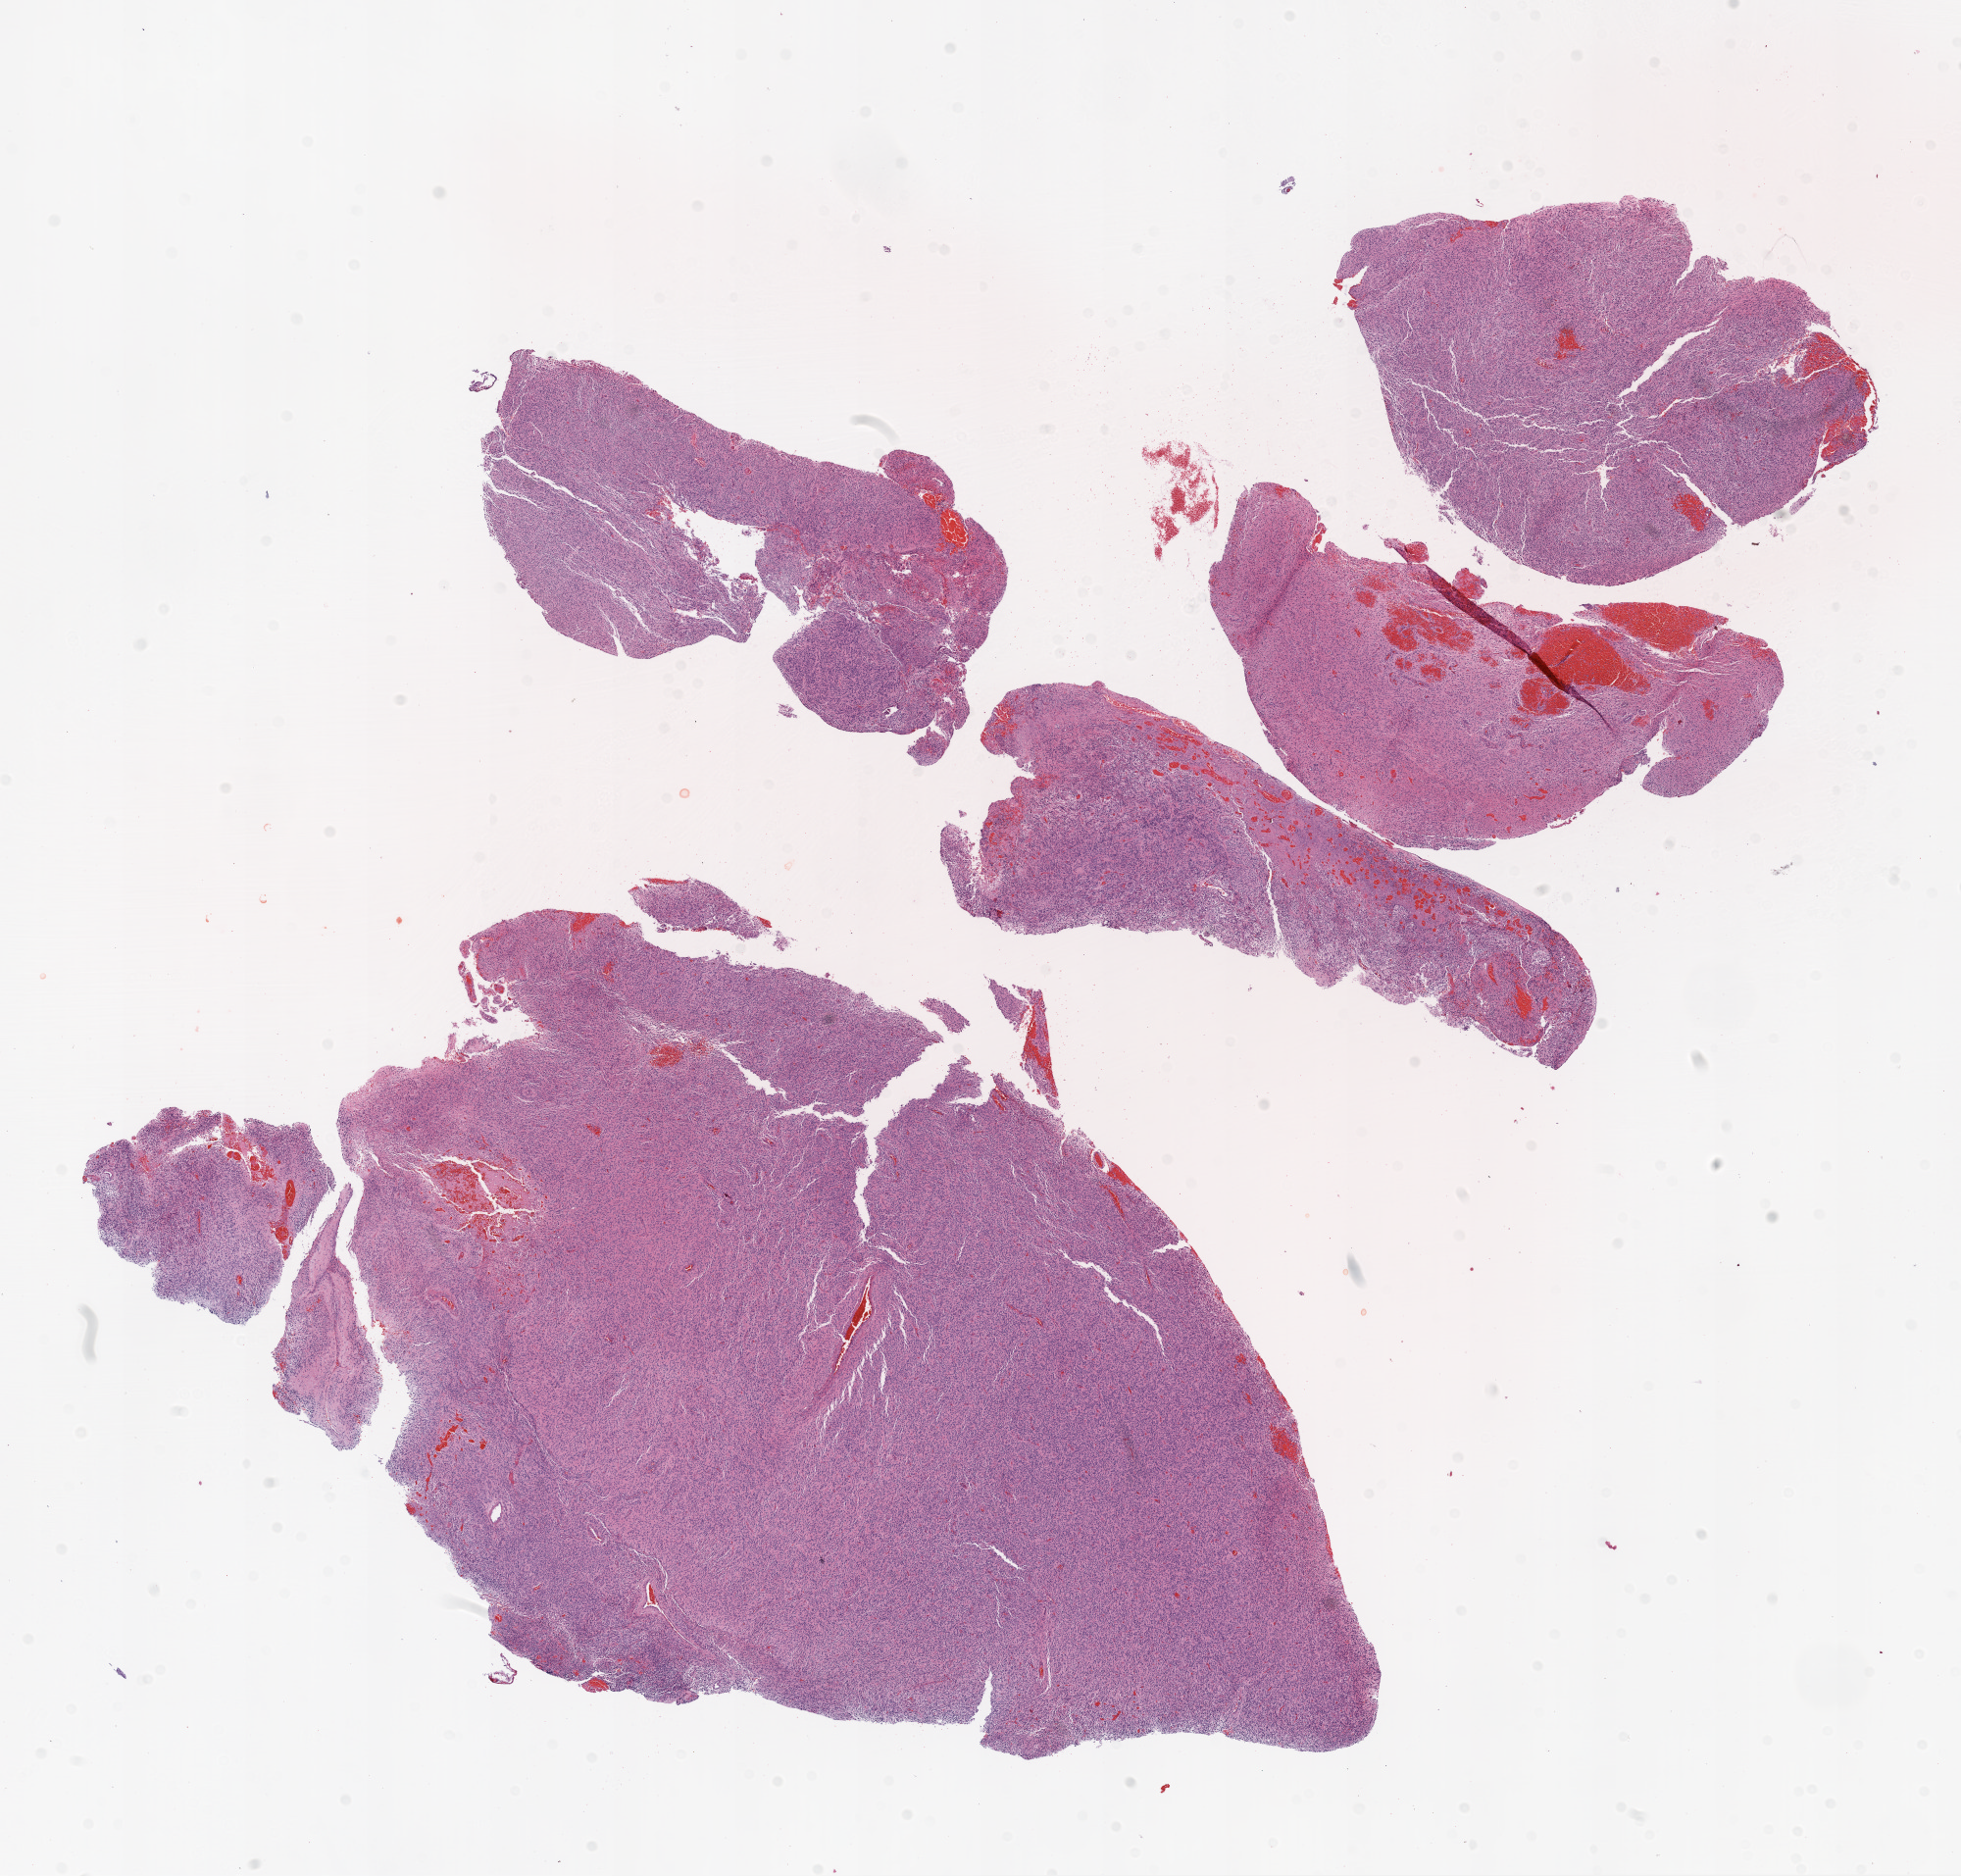
Hematoxylin and eosin (H&E) stained whole-slide image, whole scanned area (about 16.0 x 15.4 mm, acquisition: 20x scan) shown as a low-resolution overview. FFPE section. Sample: primary tumour, brain. Male patient; age at initial diagnosis 53 years.
- pathologic diagnosis: Glioblastoma